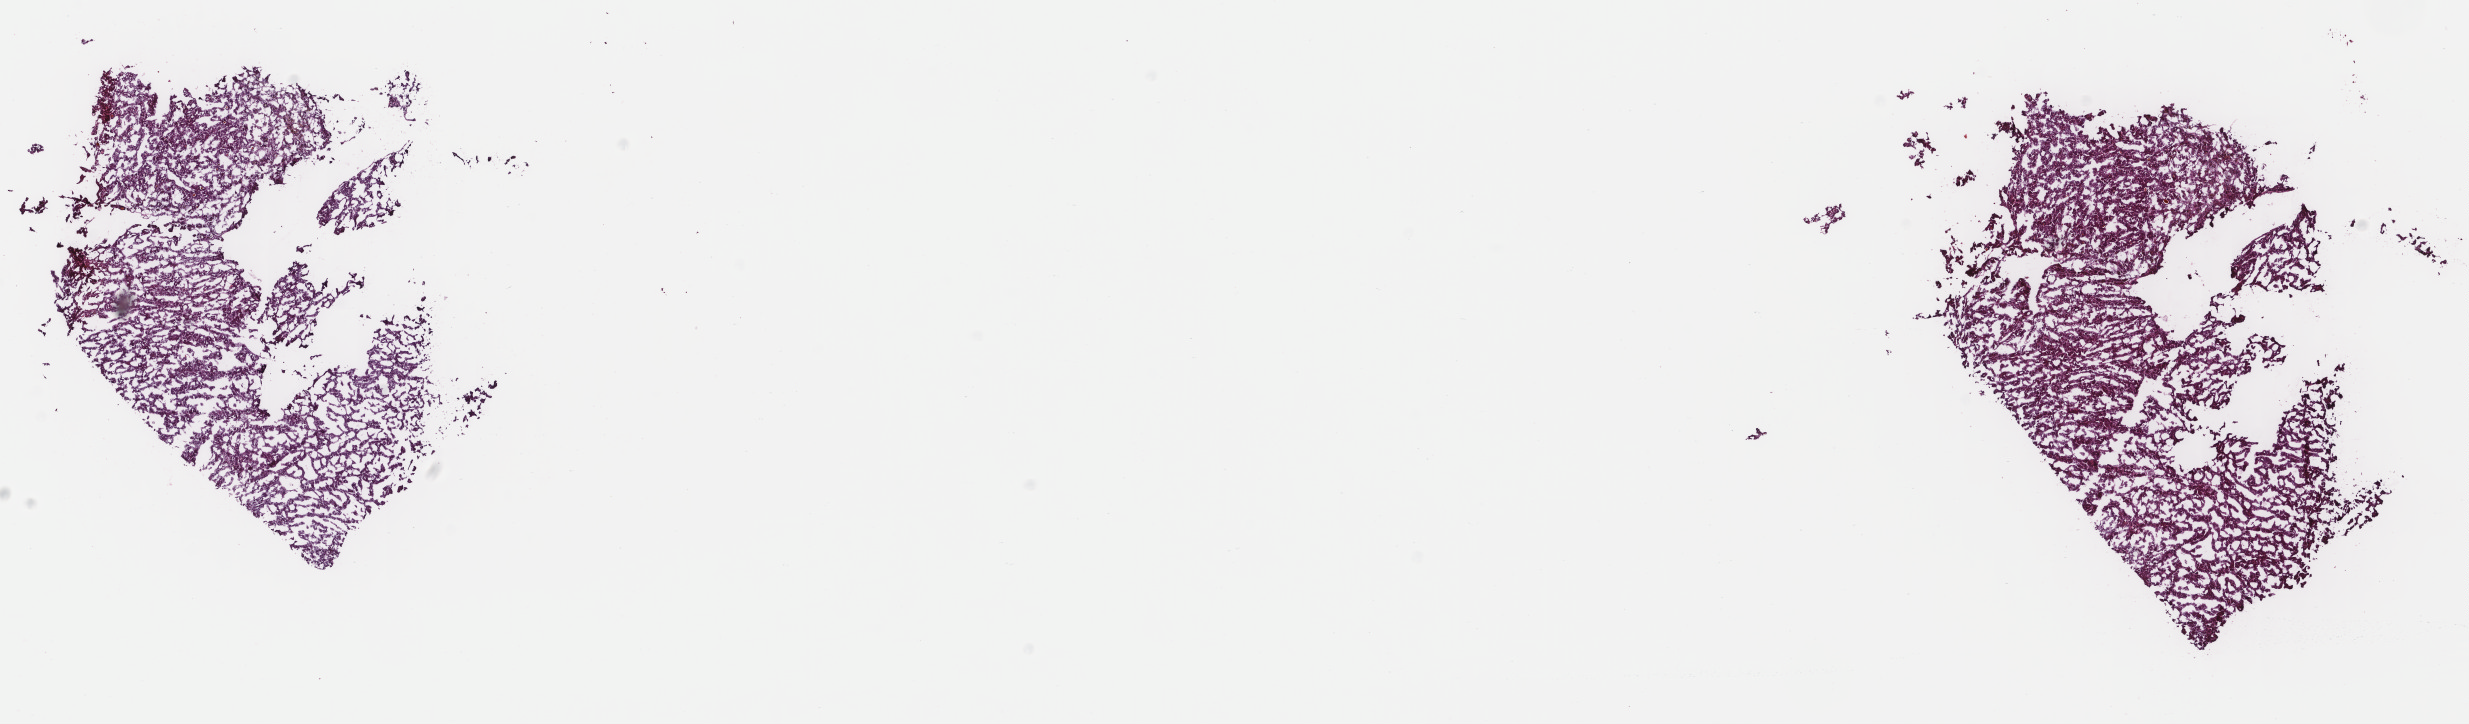
Whole-slide histology image, Hematoxylin and eosin (H&E) stained, low-resolution overview of the scanned area, about 19.6 x 5.7 mm; frozen section from the top of the tissue portion; liver, primary tumour sample. Patient: male, age at initial diagnosis 75 years. Histologic grade: G2 (moderately differentiated). Composition of this section per pathologist review: tumour cells 90%, tumour nuclei 90%, normal cells 0%, stromal cells 10%, necrosis 0%. Inflammatory infiltration, as recorded: lymphocyte infiltration 0%, monocyte infiltration 0%, neutrophil infiltration 0%.
AJCC pathologic stage: II (5th edition). Pathologic diagnosis: Hepatocellular carcinoma, NOS.